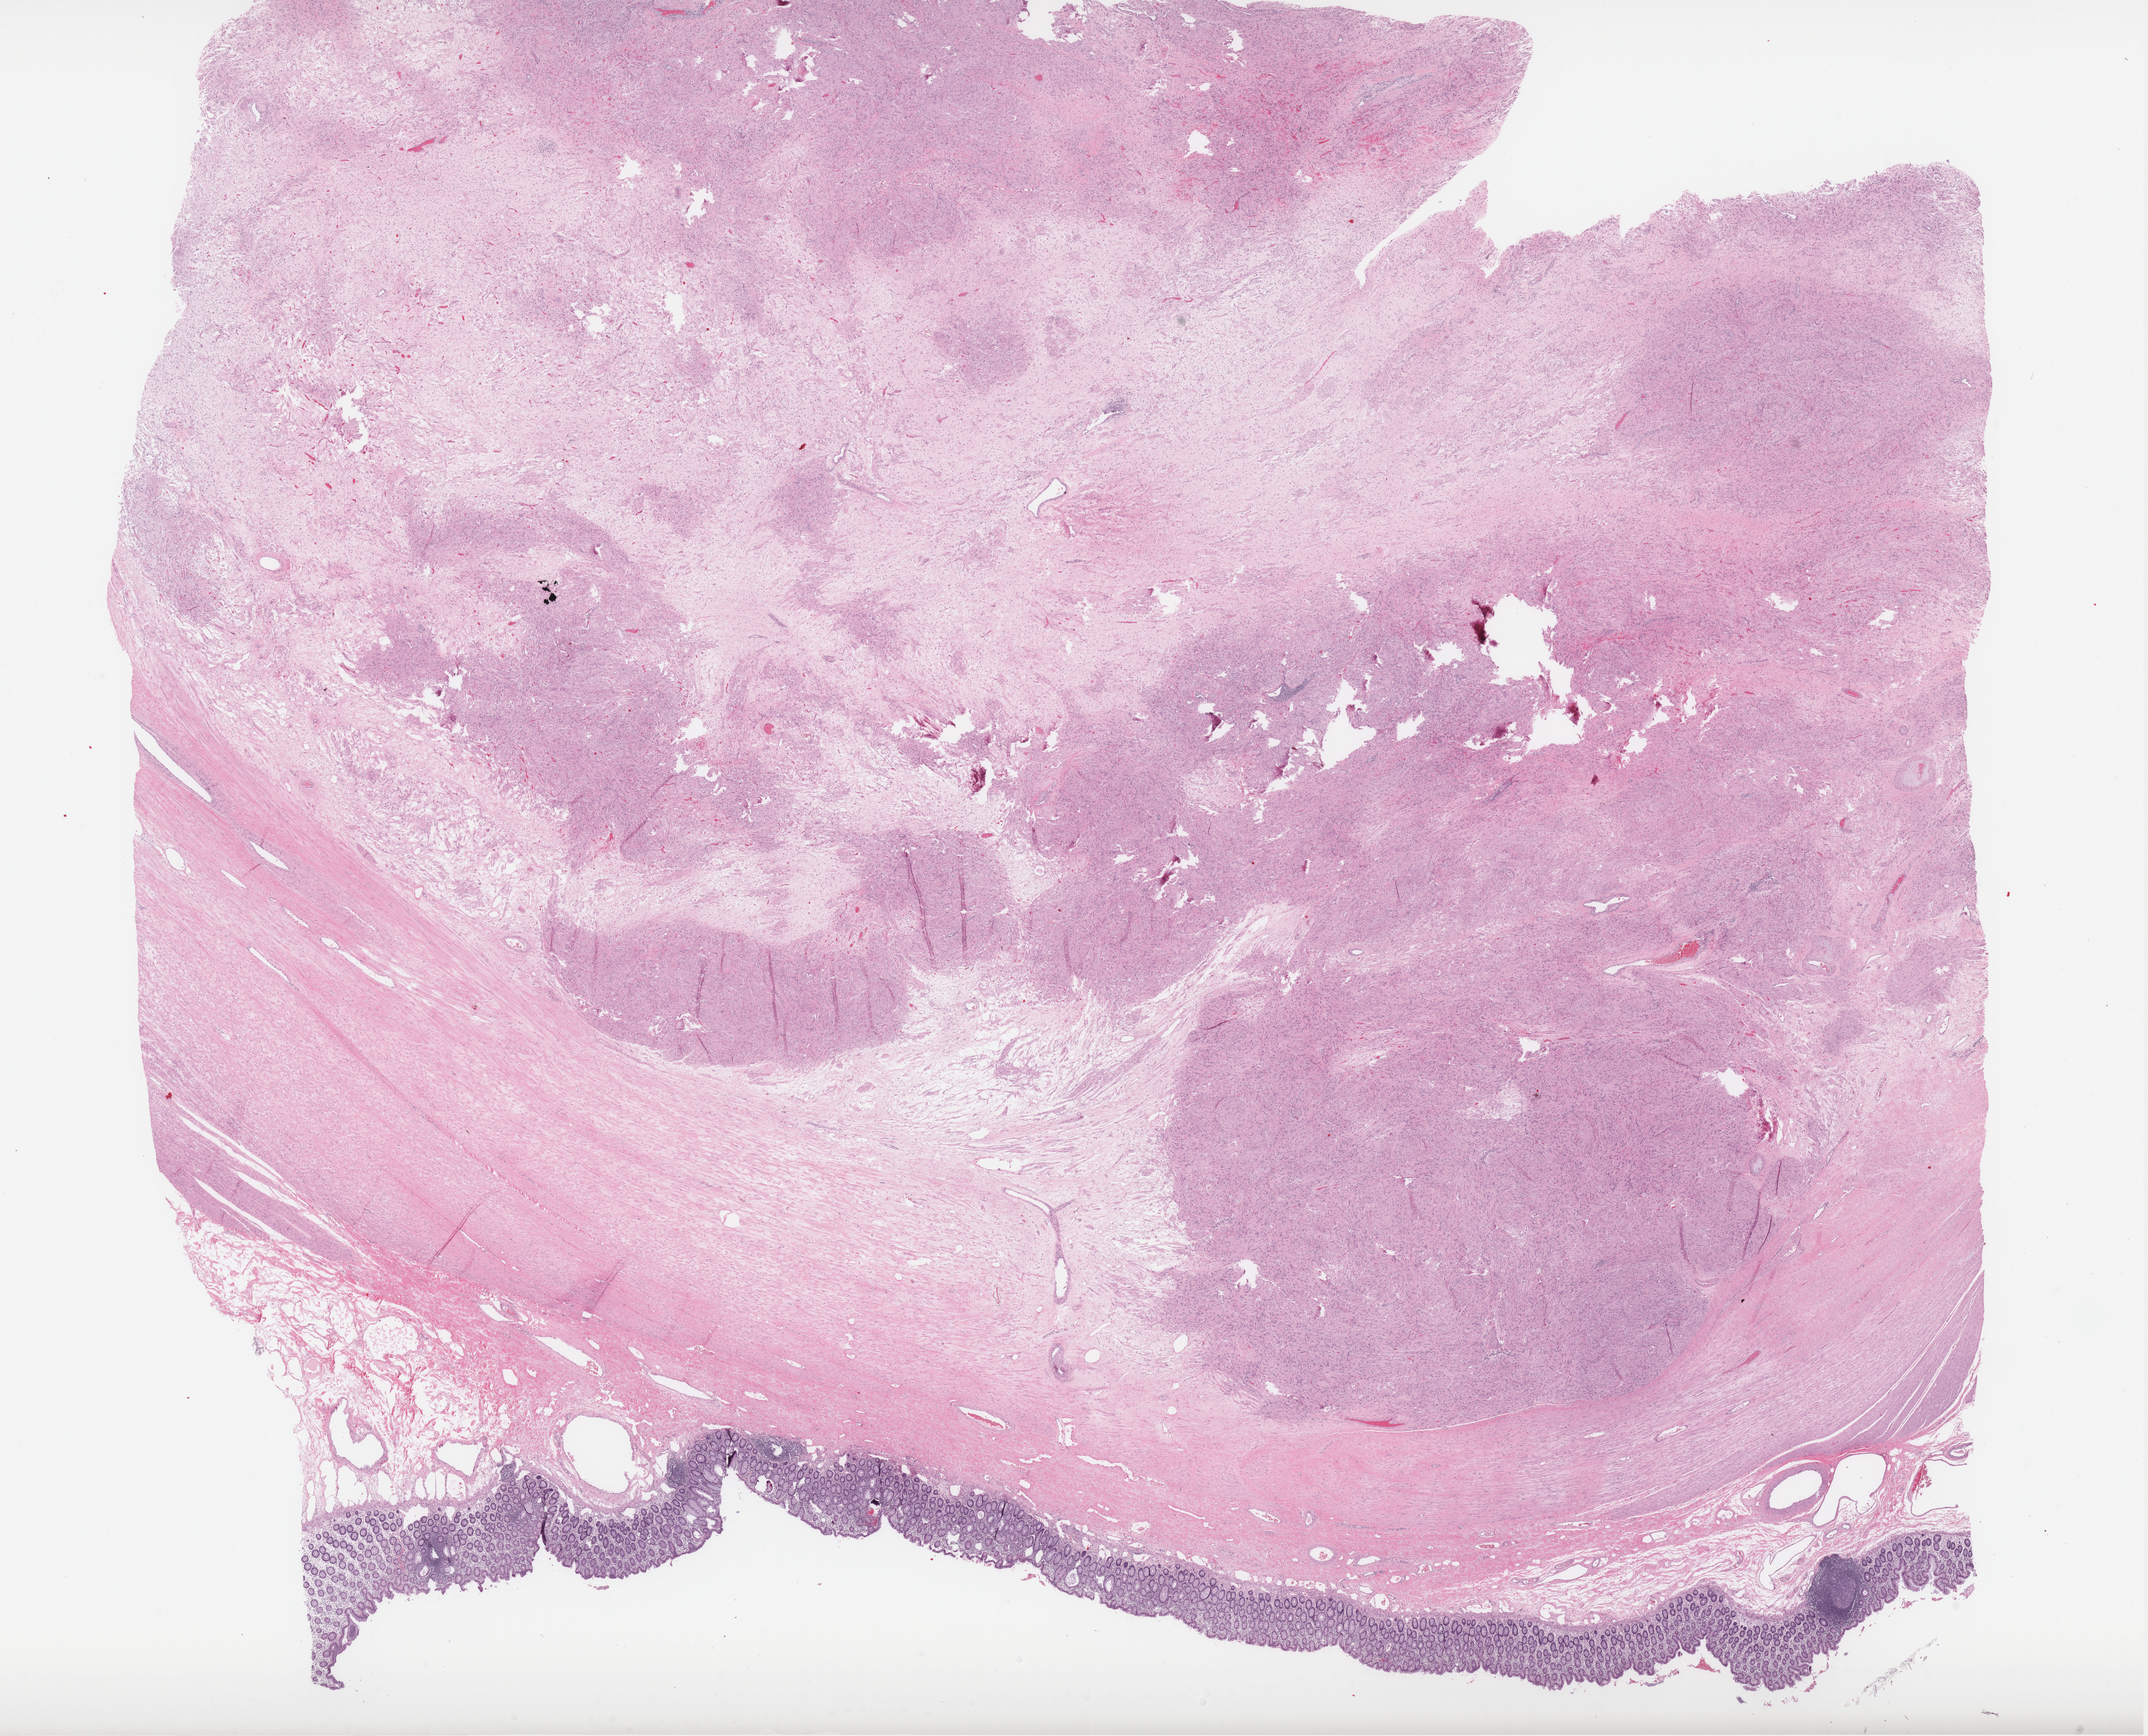
Hematoxylin and eosin (H&E) stained whole-slide image, low-resolution overview of the scanned area, about 26.2 x 21.1 mm (slide scanned at 40x), formalin-fixed paraffin-embedded (FFPE) diagnostic section, sample: primary tumour, connective, subcutaneous and other soft tissues. Patient: female, age at initial diagnosis 45 years.
Histologic diagnosis: Leiomyosarcoma, NOS (overlapping lesion of connective, subcutaneous and other soft tissues).